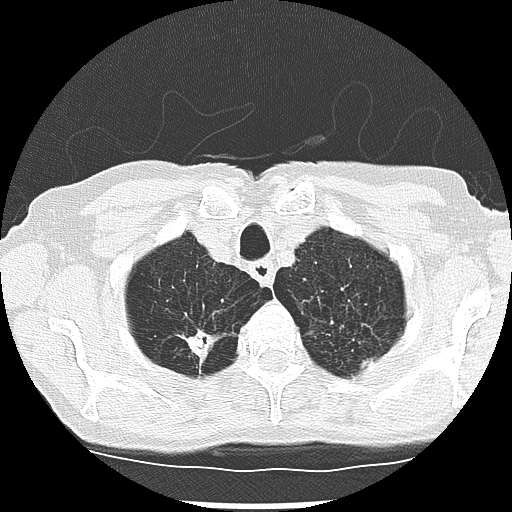
Low-dose screening chest CT, one axial slice; slice 238 of 265 in the series (ordered by position); reconstruction kernel LUNG; 120 kVp; lung window (W 1500 / L -600 HU); 2.5 mm slice thickness; 512 × 512 image matrix, field of view 300 × 300 mm.
Outlined on this slice (manually delineated by an expert):
- lesion 2 (tumor, upper lobe of right lung): box from (x=182, y=330) to (x=217, y=362) px